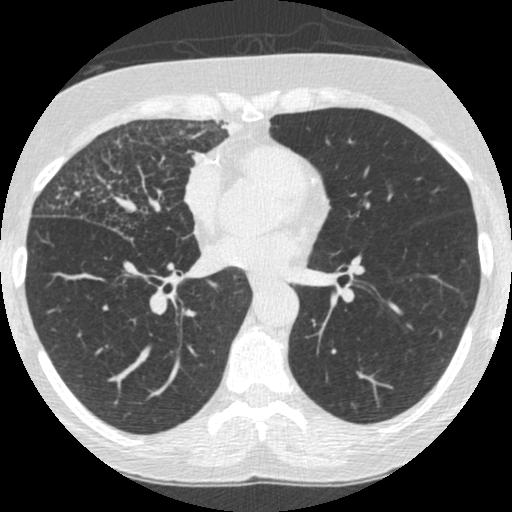
Low-dose screening chest CT, one axial slice; slice 124 of 253 in the series (ordered by position); reconstruction kernel STANDARD; 120 kVp; lung window (W 1500 / L -600 HU); 1.25 mm slice thickness; 512 × 512 image matrix, field of view 294 × 294 mm.
Structures marked on this image (expert manual segmentation):
- lesion 4 (tumor, upper lobe of right lung): bounding box <193,117,242,155> (left, top, right, bottom; pixels)